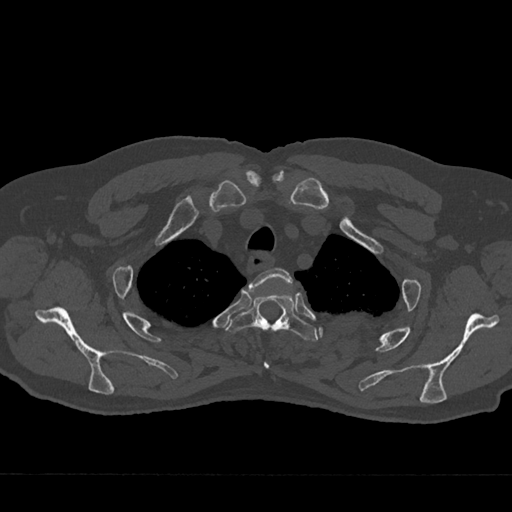
CT including the spine, one axial slice; 120 kVp; bone window (W 1800 / L 400 HU); 0.5 mm slice thickness; 512 × 512 image matrix. Patient: male, 75 years. Case-level facts recorded for this patient, not image findings: primary cancer: renal; vertebrae with lytic lesions (as recorded): T4.
Annotated regions visible in this slice (semi-automatically segmented with operator editing):
- T2 vertebra: bounding box (x1, y1, x2, y2) in pixels: (249, 268, 293, 368)
- T3 vertebra: (228, 292, 318, 342)